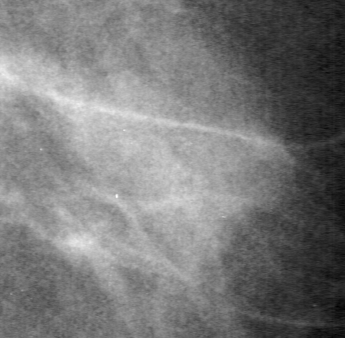
Region of interest cut from a scanned film mammogram (one marked finding), right breast, MLO view.
Mass, shape oval, margins ill defined; BI-RADS assessment category 4; subtlety rating 4 on a 1 (subtle) to 5 (obvious) scale; pathology result (as recorded, not read from the image): malignant.